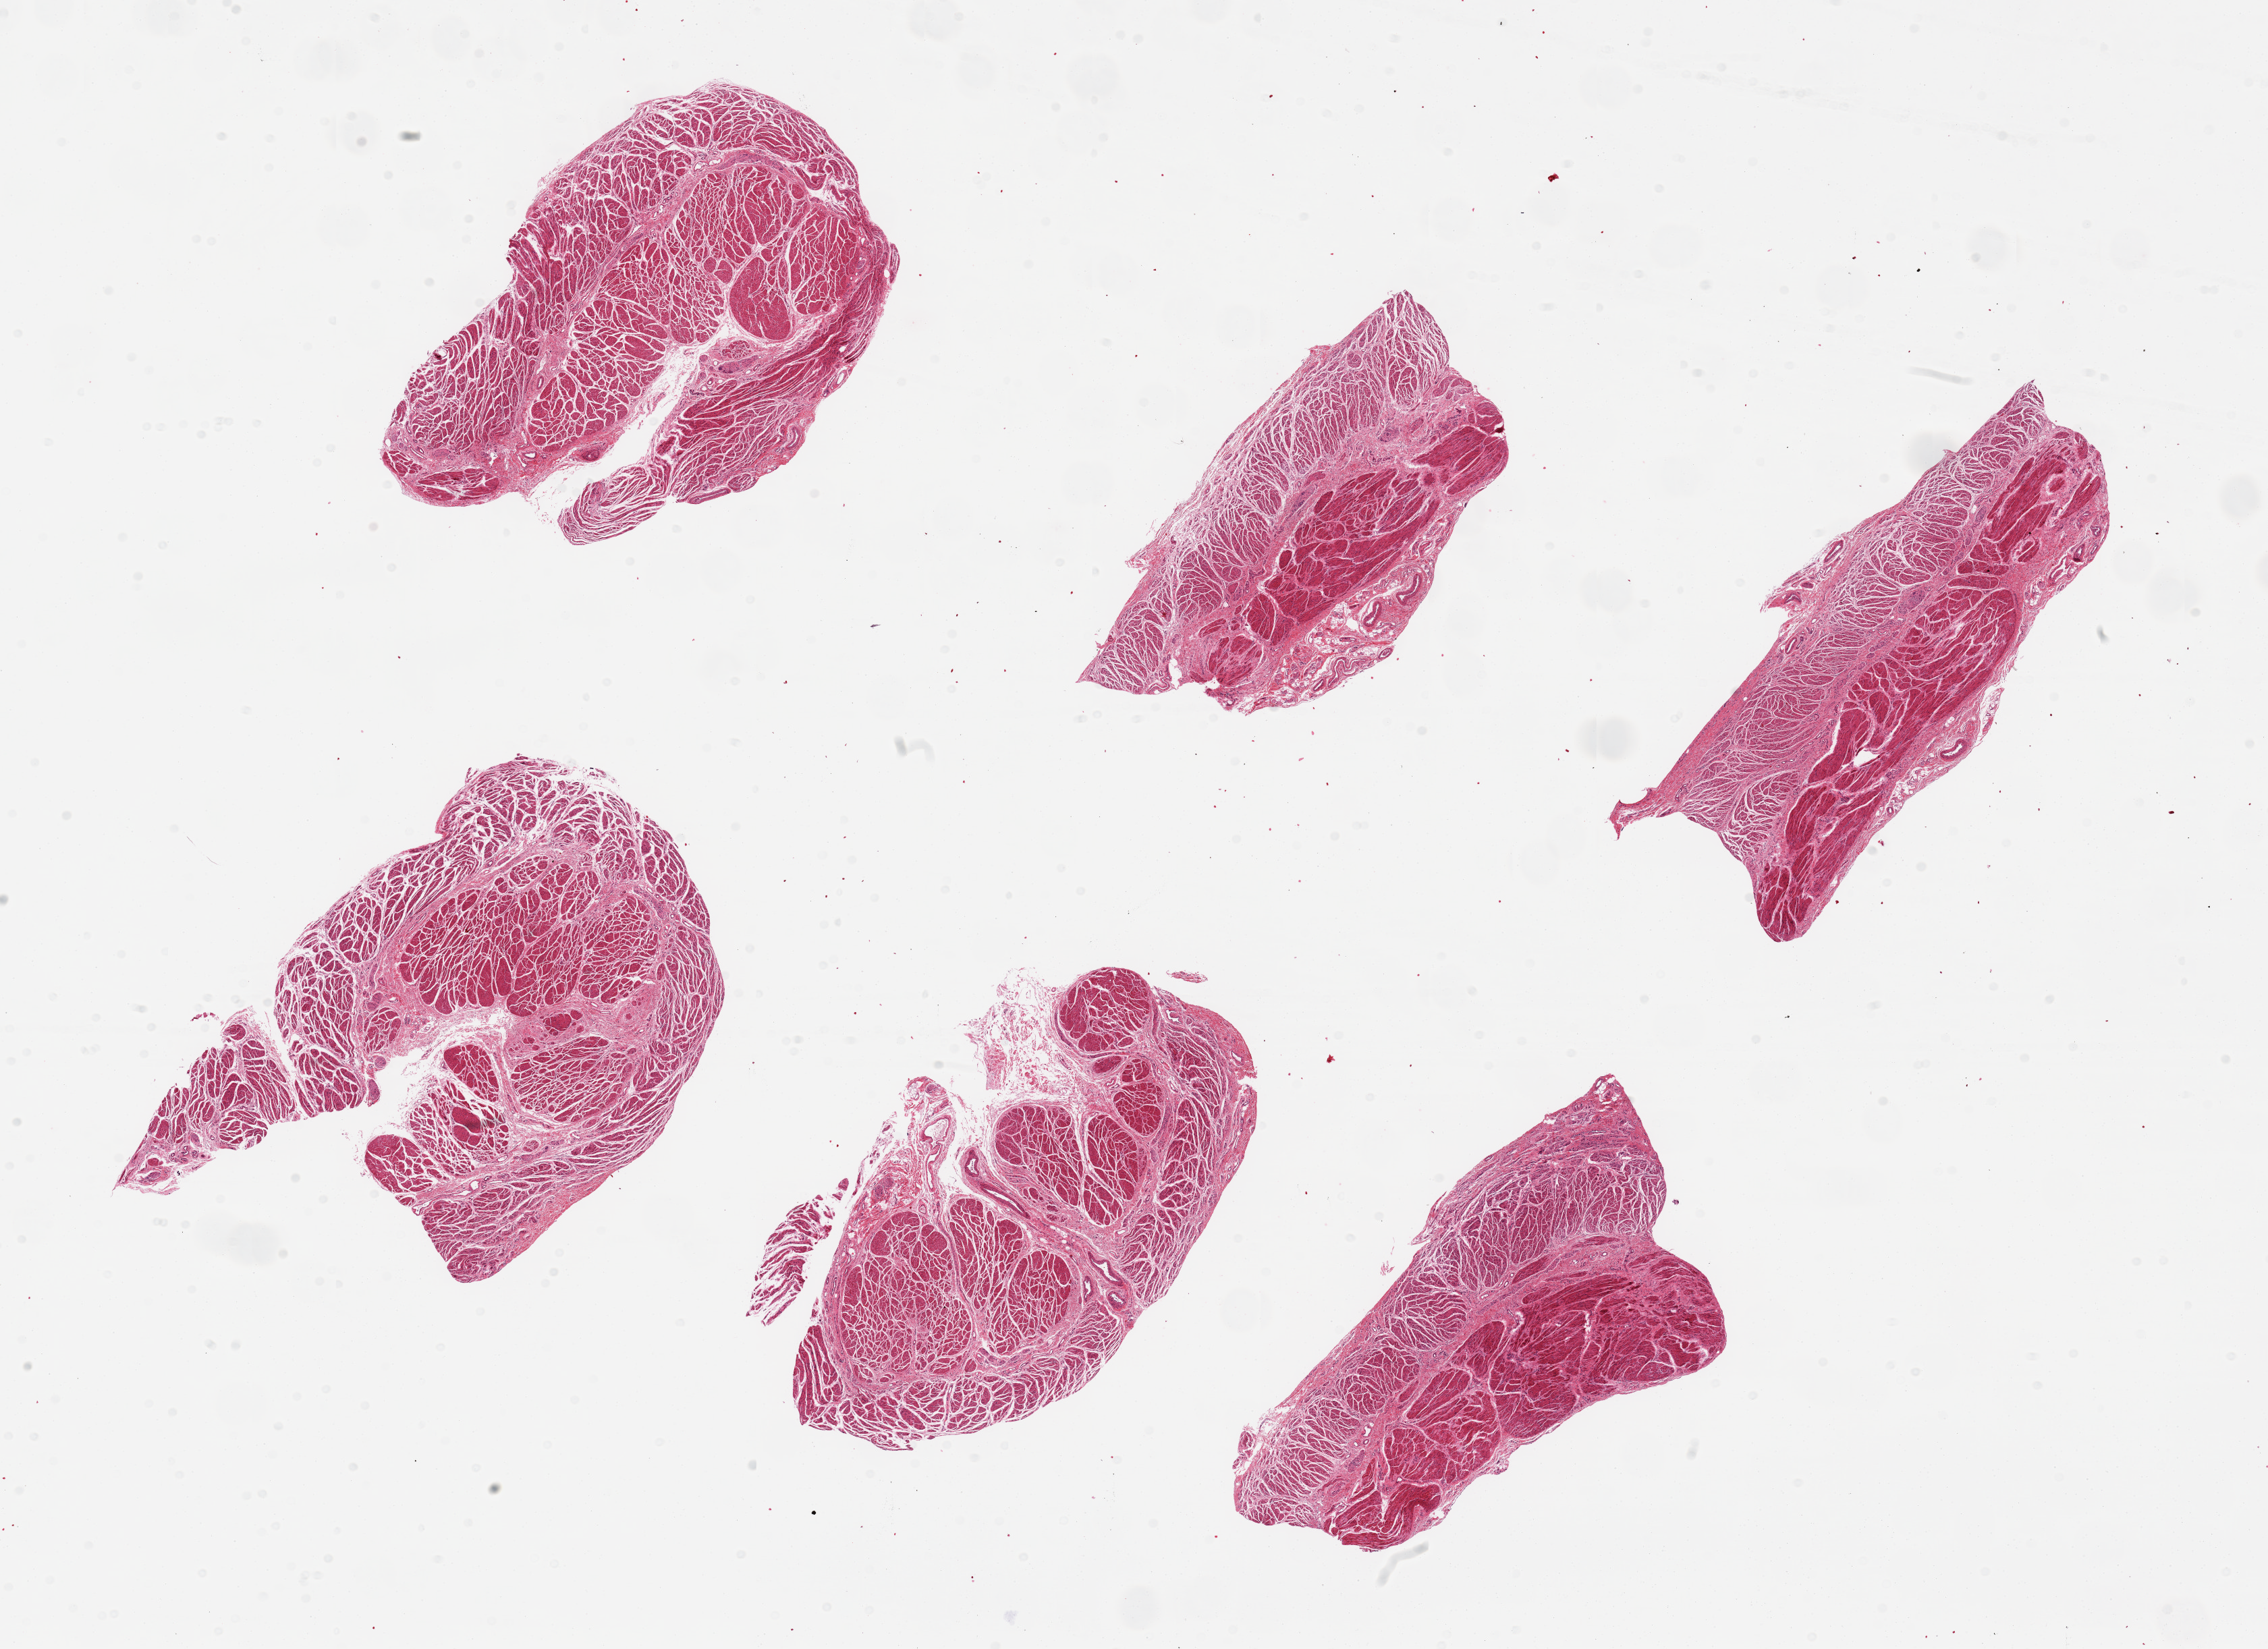
Digitized haematoxylin and eosin-stained section — whole scanned area (about 26.6 x 19.3 mm) shown as a low-resolution overview. PAXgene-fixed, paraffin-embedded tissue. Section of gastroesophageal junction (target tissue). Tissue donor sample. Male donor.
• reviewer comment on this tissue sample: 5 pieces, well trimmed